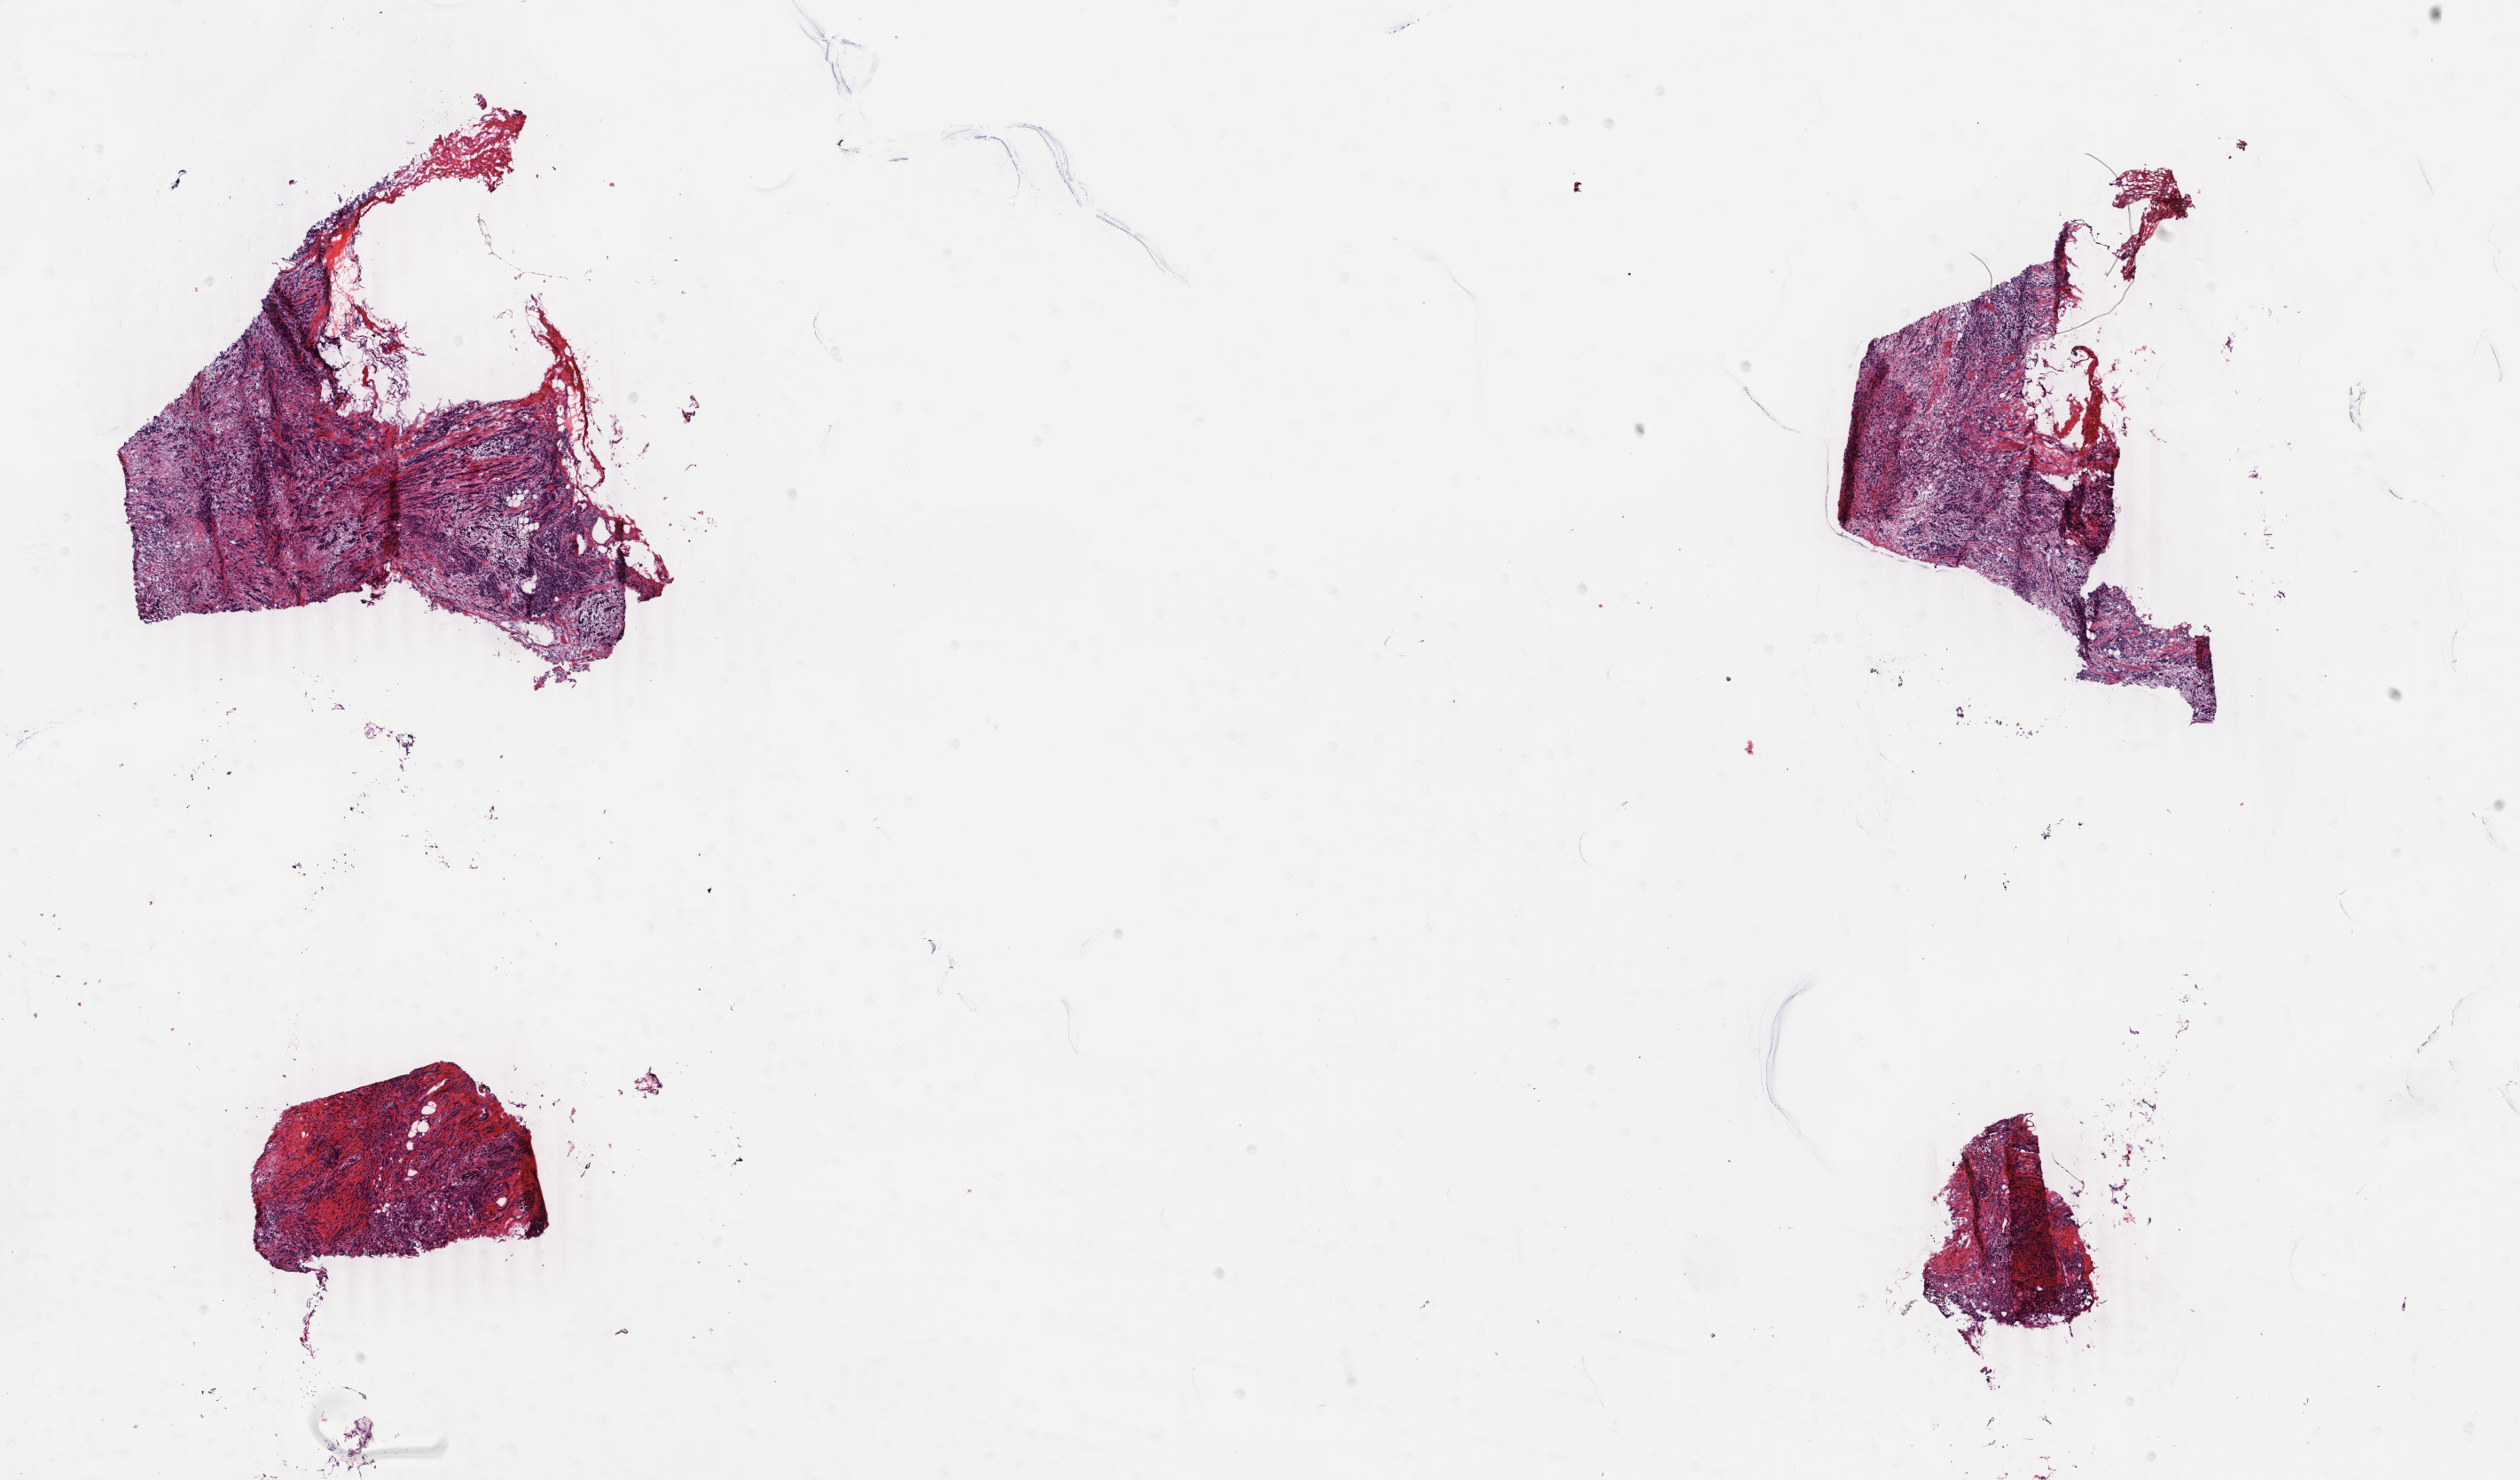
Whole-slide histology image, Hematoxylin and eosin (H&E) stained — a low-resolution overview of the entire scanned area, about 22.6 x 13.3 mm (slide scanned at 40x), frozen section, primary tumour sample from the breast. Female patient; age at initial diagnosis 61 years. Slide review estimates, as recorded: tumour cells 85%, tumour nuclei 85%, normal cells 0%, stromal cells 15%, necrosis 0%. Infiltration values recorded for this section: lymphocyte infiltration 2%, monocyte infiltration 0%, neutrophil infiltration 0%.
Lymph nodes positive (case pathology): 15 of 32 examined. AJCC pathologic stage: IIIC. Diagnosis: Lobular carcinoma, NOS.